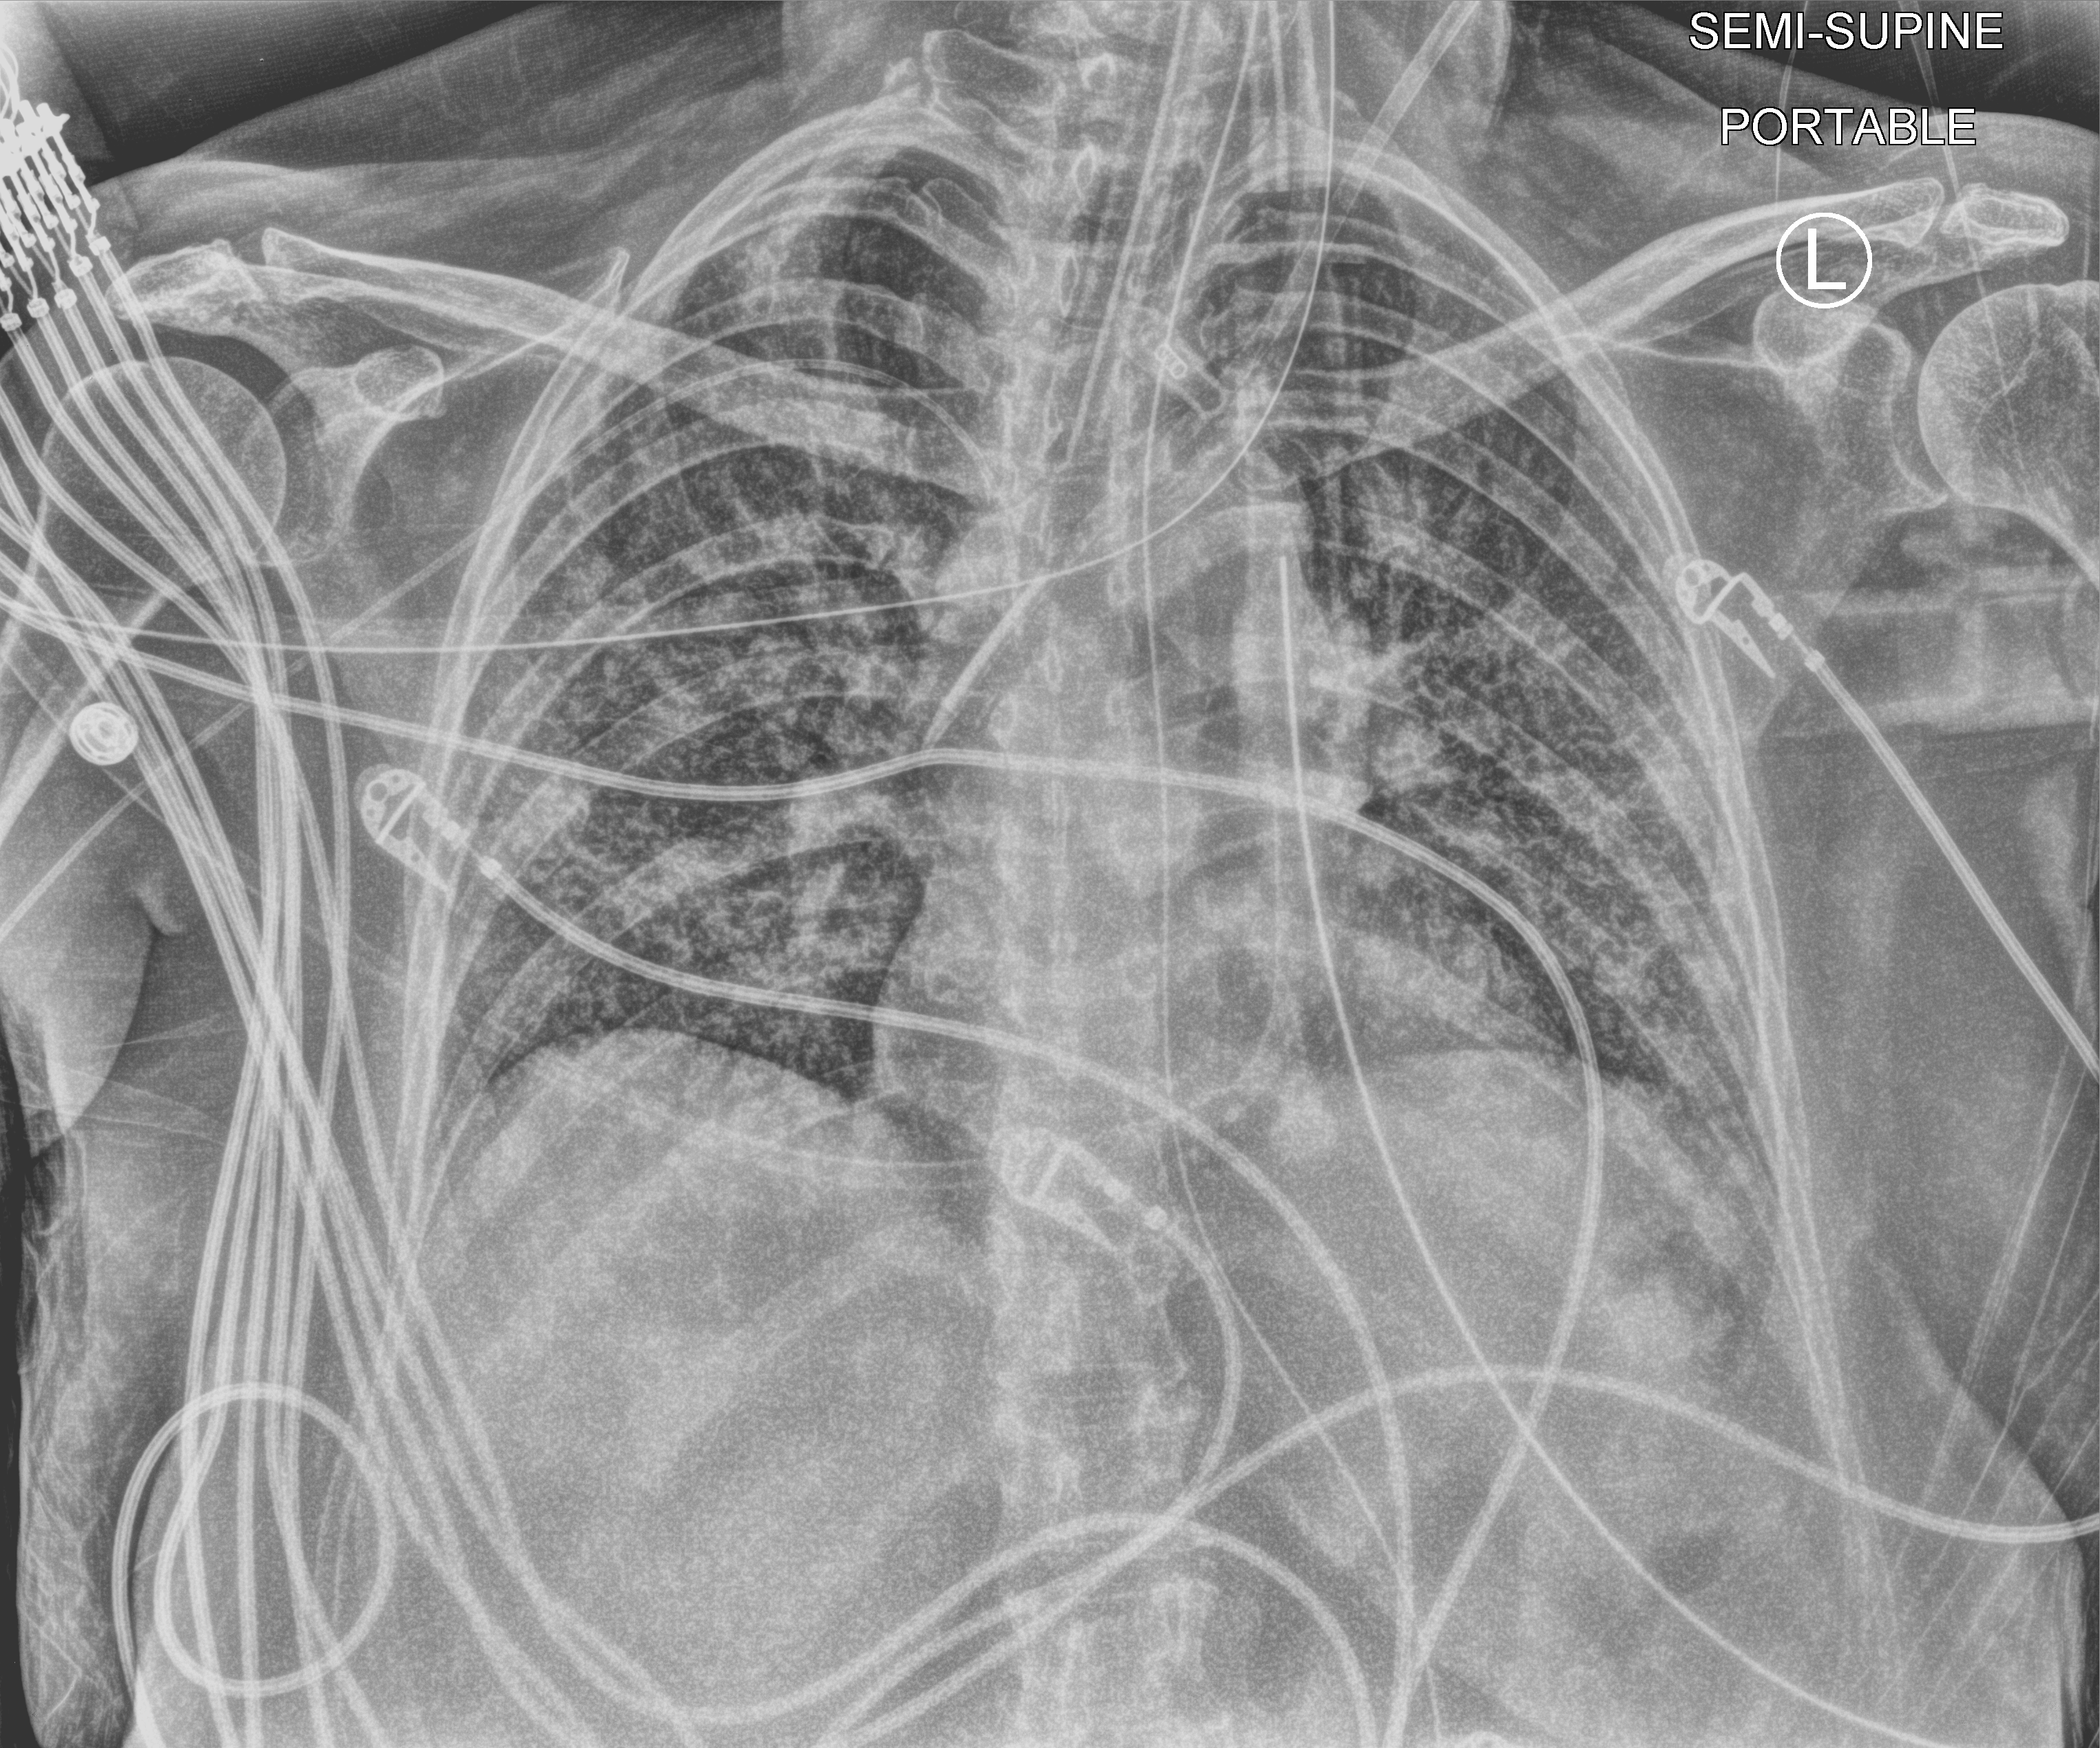
Portable chest radiograph, anteroposterior (AP) projection. Female patient hospitalised with COVID-19, age 60–74 years.
From the hospital-stay record, not from the radiograph (when in the stay this image was taken is not recorded):
- admitted to intensive care during this hospital stay: yes